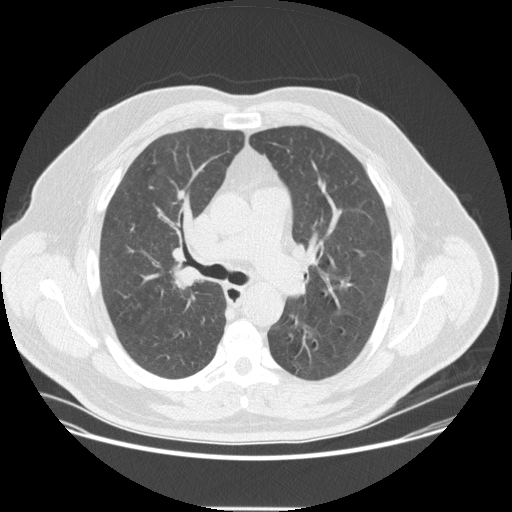
Low-dose screening chest CT, one axial slice. Position 224 of 351 along the scan axis. 120 kVp. Lung window (W 1500 / L -600 HU). 2.5 mm slice thickness. 512 × 512 image matrix, field of view 419 × 419 mm.
Structures marked on this image (manually delineated by an expert):
- lesion 1 (tumor, upper lobe of right lung): bounding box (x1, y1, x2, y2) in pixels: (173, 271, 201, 289)